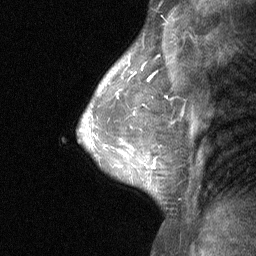
Breast MRI (dynamic contrast-enhanced), one sagittal slice. Dynamic contrast-enhanced study with each time point stored as its own series, time point 2 of 3 at this slice position (early post-contrast, ordered by acquisition time). 1.5 T. TE 4.8 ms, TR 27 ms. 2 mm slice thickness. 256 × 256 image matrix, field of view 180 × 180 mm. Patient: female, 47 years. Case-level facts recorded for this patient, not image findings: setting: breast cancer imaged before/during neoadjuvant chemotherapy; receptor status: HR-positive, HER2-negative.
Outlined on this slice (semi-automatically segmented with operator editing):
- analysis volume of interest (the breast-tissue region the enhancement analysis was run in; not a lesion): bounding box <104,138,165,198> (left, top, right, bottom; pixels)
- tumour enhancement mask (voxels above the 90 % enhancement threshold inside the analysis volume of interest): <151,160,156,169>